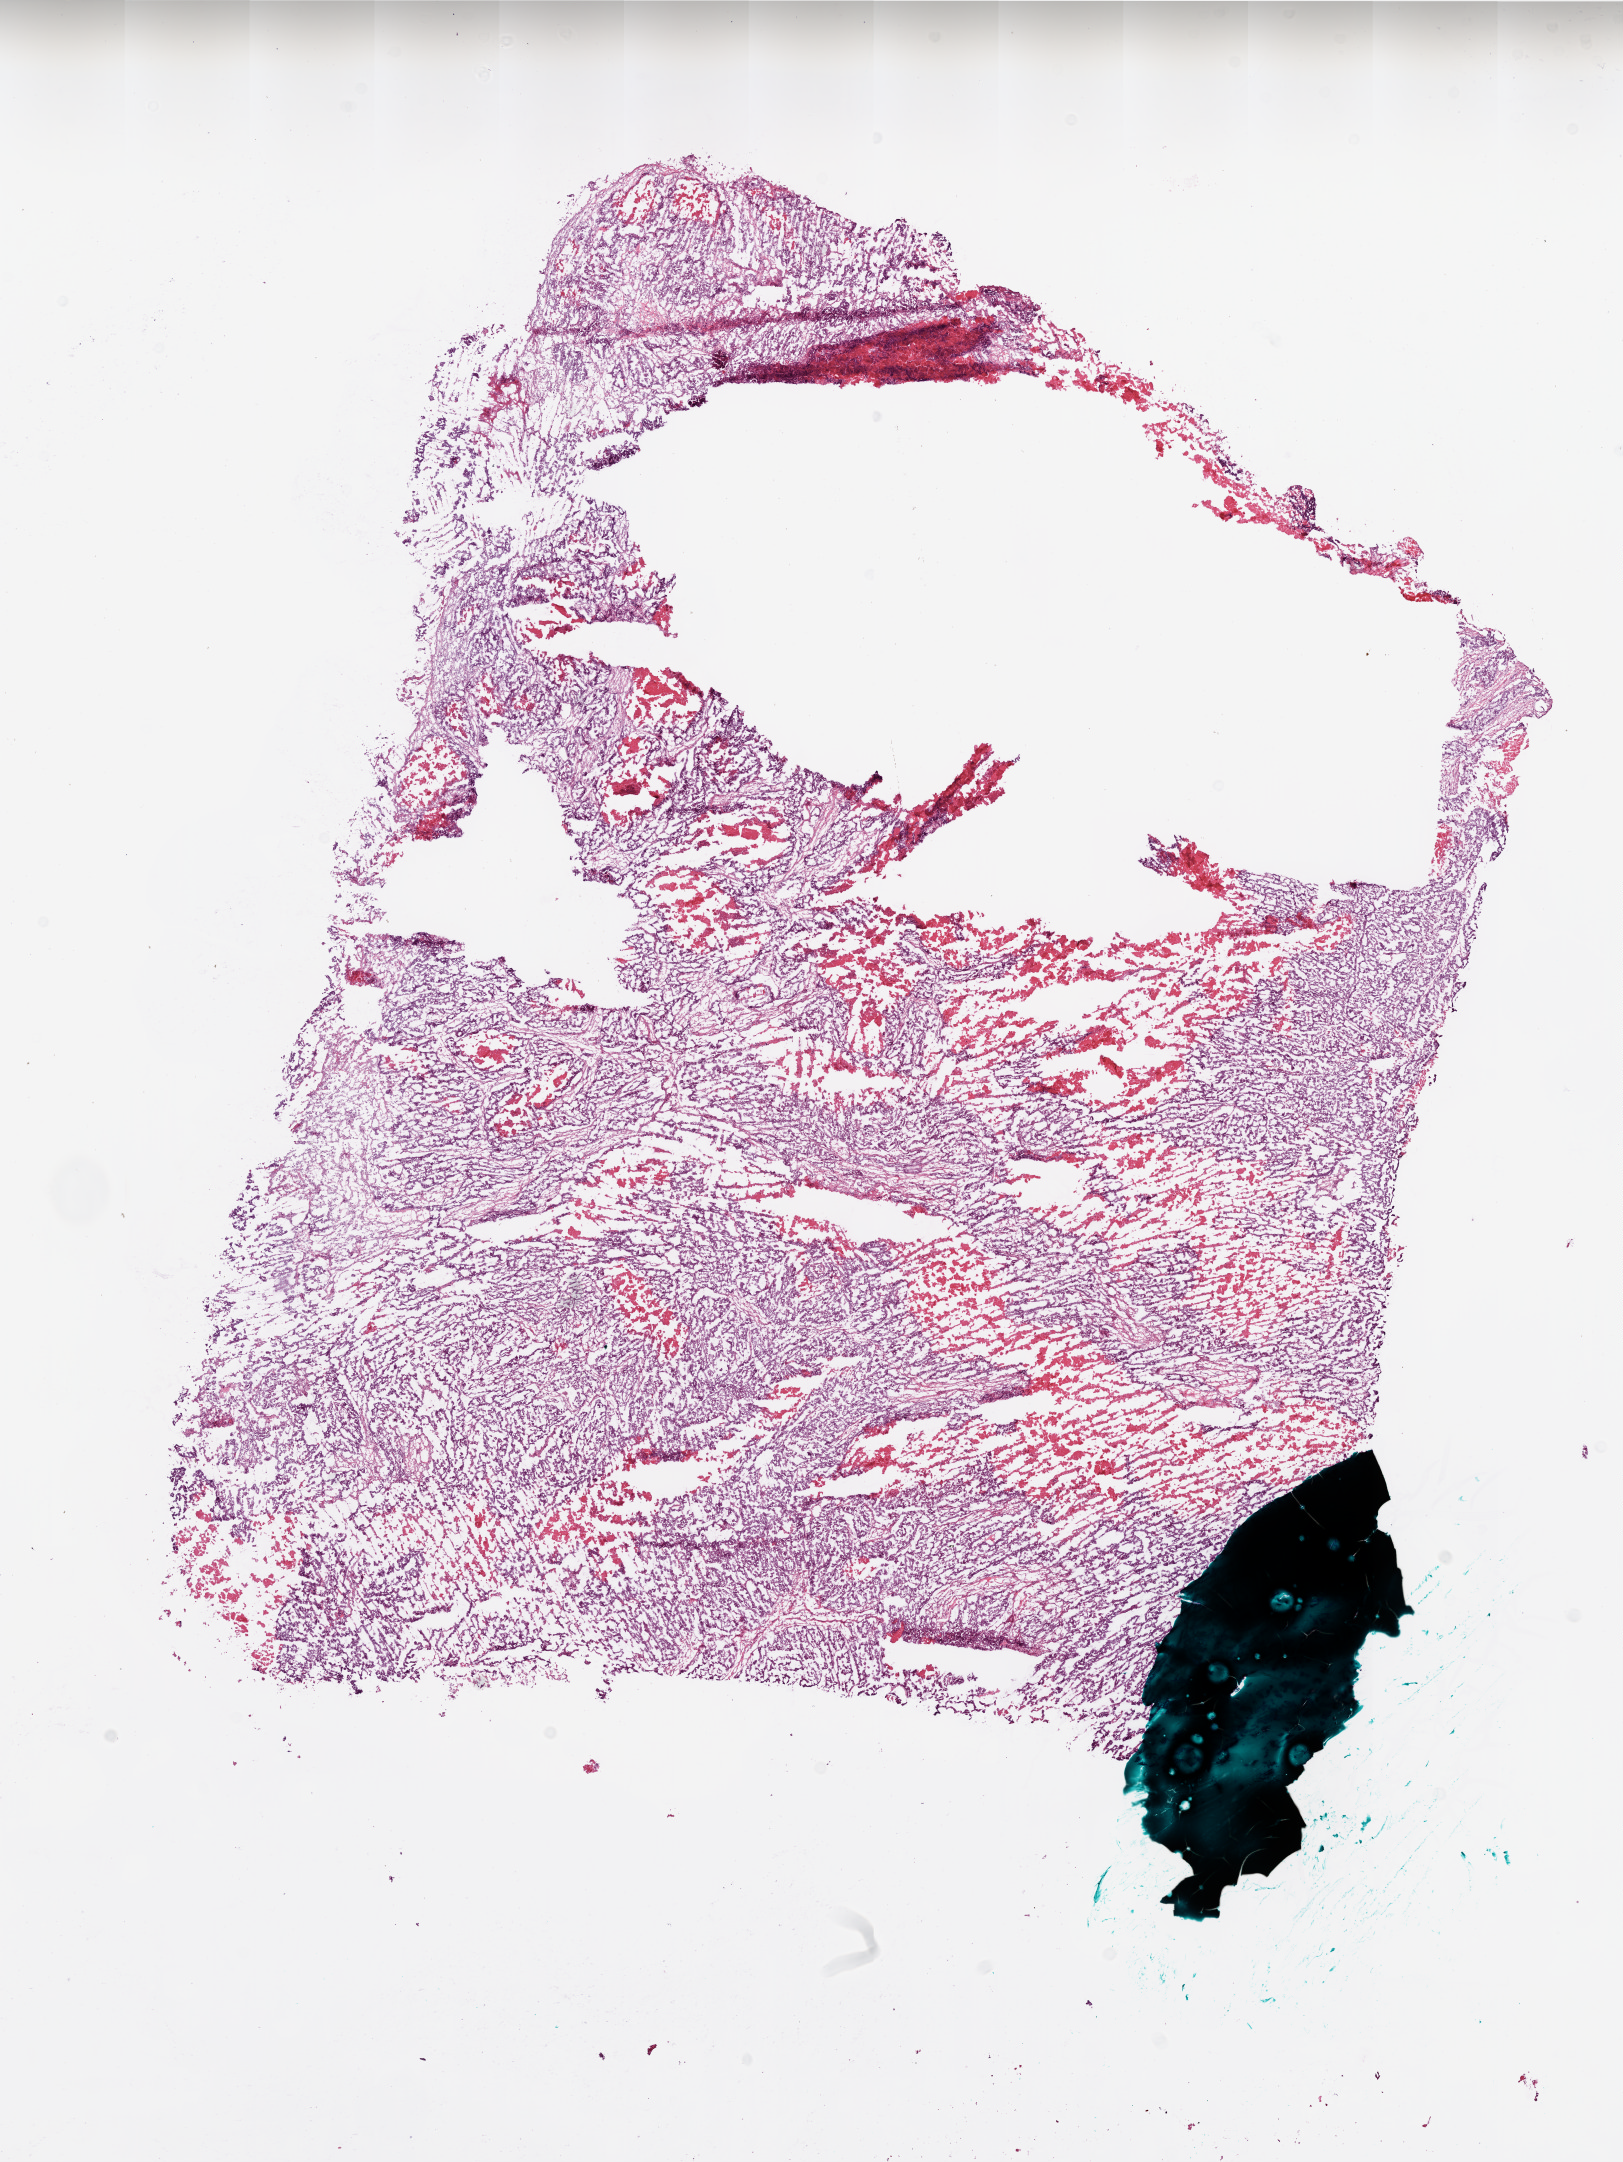
Digitized Hematoxylin and eosin (H&E) stained tissue section (whole slide) — whole scanned area (about 13.0 x 17.3 mm, from a 20x scan) shown as a low-resolution overview, frozen section, sample: primary tumour, ovary. Female patient; age at initial diagnosis 42 years. Histologic grade: G3 (poorly differentiated). Pathologist review of this section (percent, as recorded): tumour cells 75%, tumour nuclei 90%, normal cells 10%, stromal cells 0%, necrosis 15%.
Pathologic diagnosis: Serous cystadenocarcinoma, NOS. FIGO stage: IV. Laterality: bilateral.